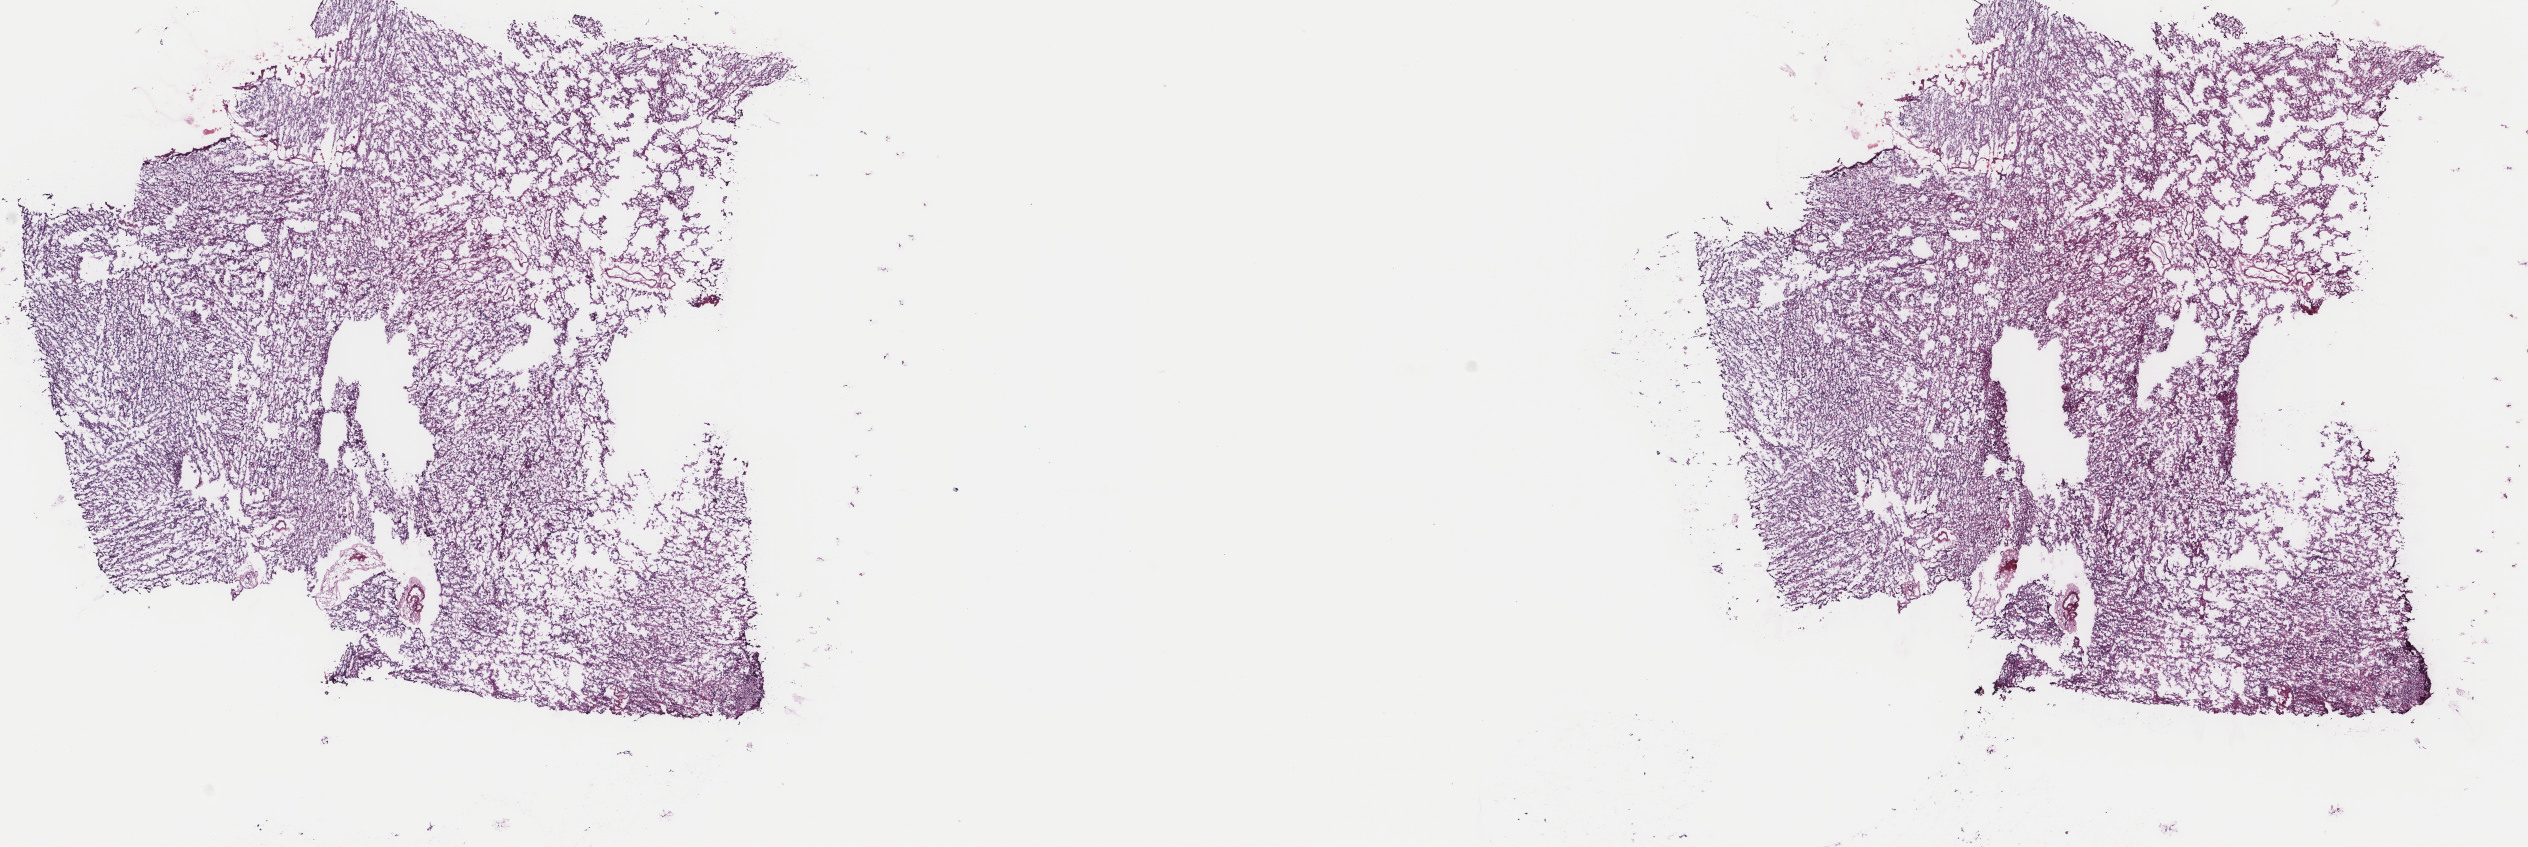
Whole-slide histology image, H&E — shown as a low-resolution overview of the whole scanned area (about 20.1 x 6.7 mm, acquisition: 40x scan); frozen section from the top of the tissue portion; sample: primary tumour, brain. Male patient; age at initial diagnosis 22 years. Histologic grade: G3 (poorly differentiated). Pathologist review of this section (percent, as recorded): tumour cells 80%, tumour nuclei 90%, normal cells 0%, stromal cells 20%, necrosis 0%. Infiltration values recorded for this section: lymphocyte infiltration 0%, monocyte infiltration 0%, neutrophil infiltration 0%.
- laterality: right
- diagnosis: Mixed glioma (cerebrum)